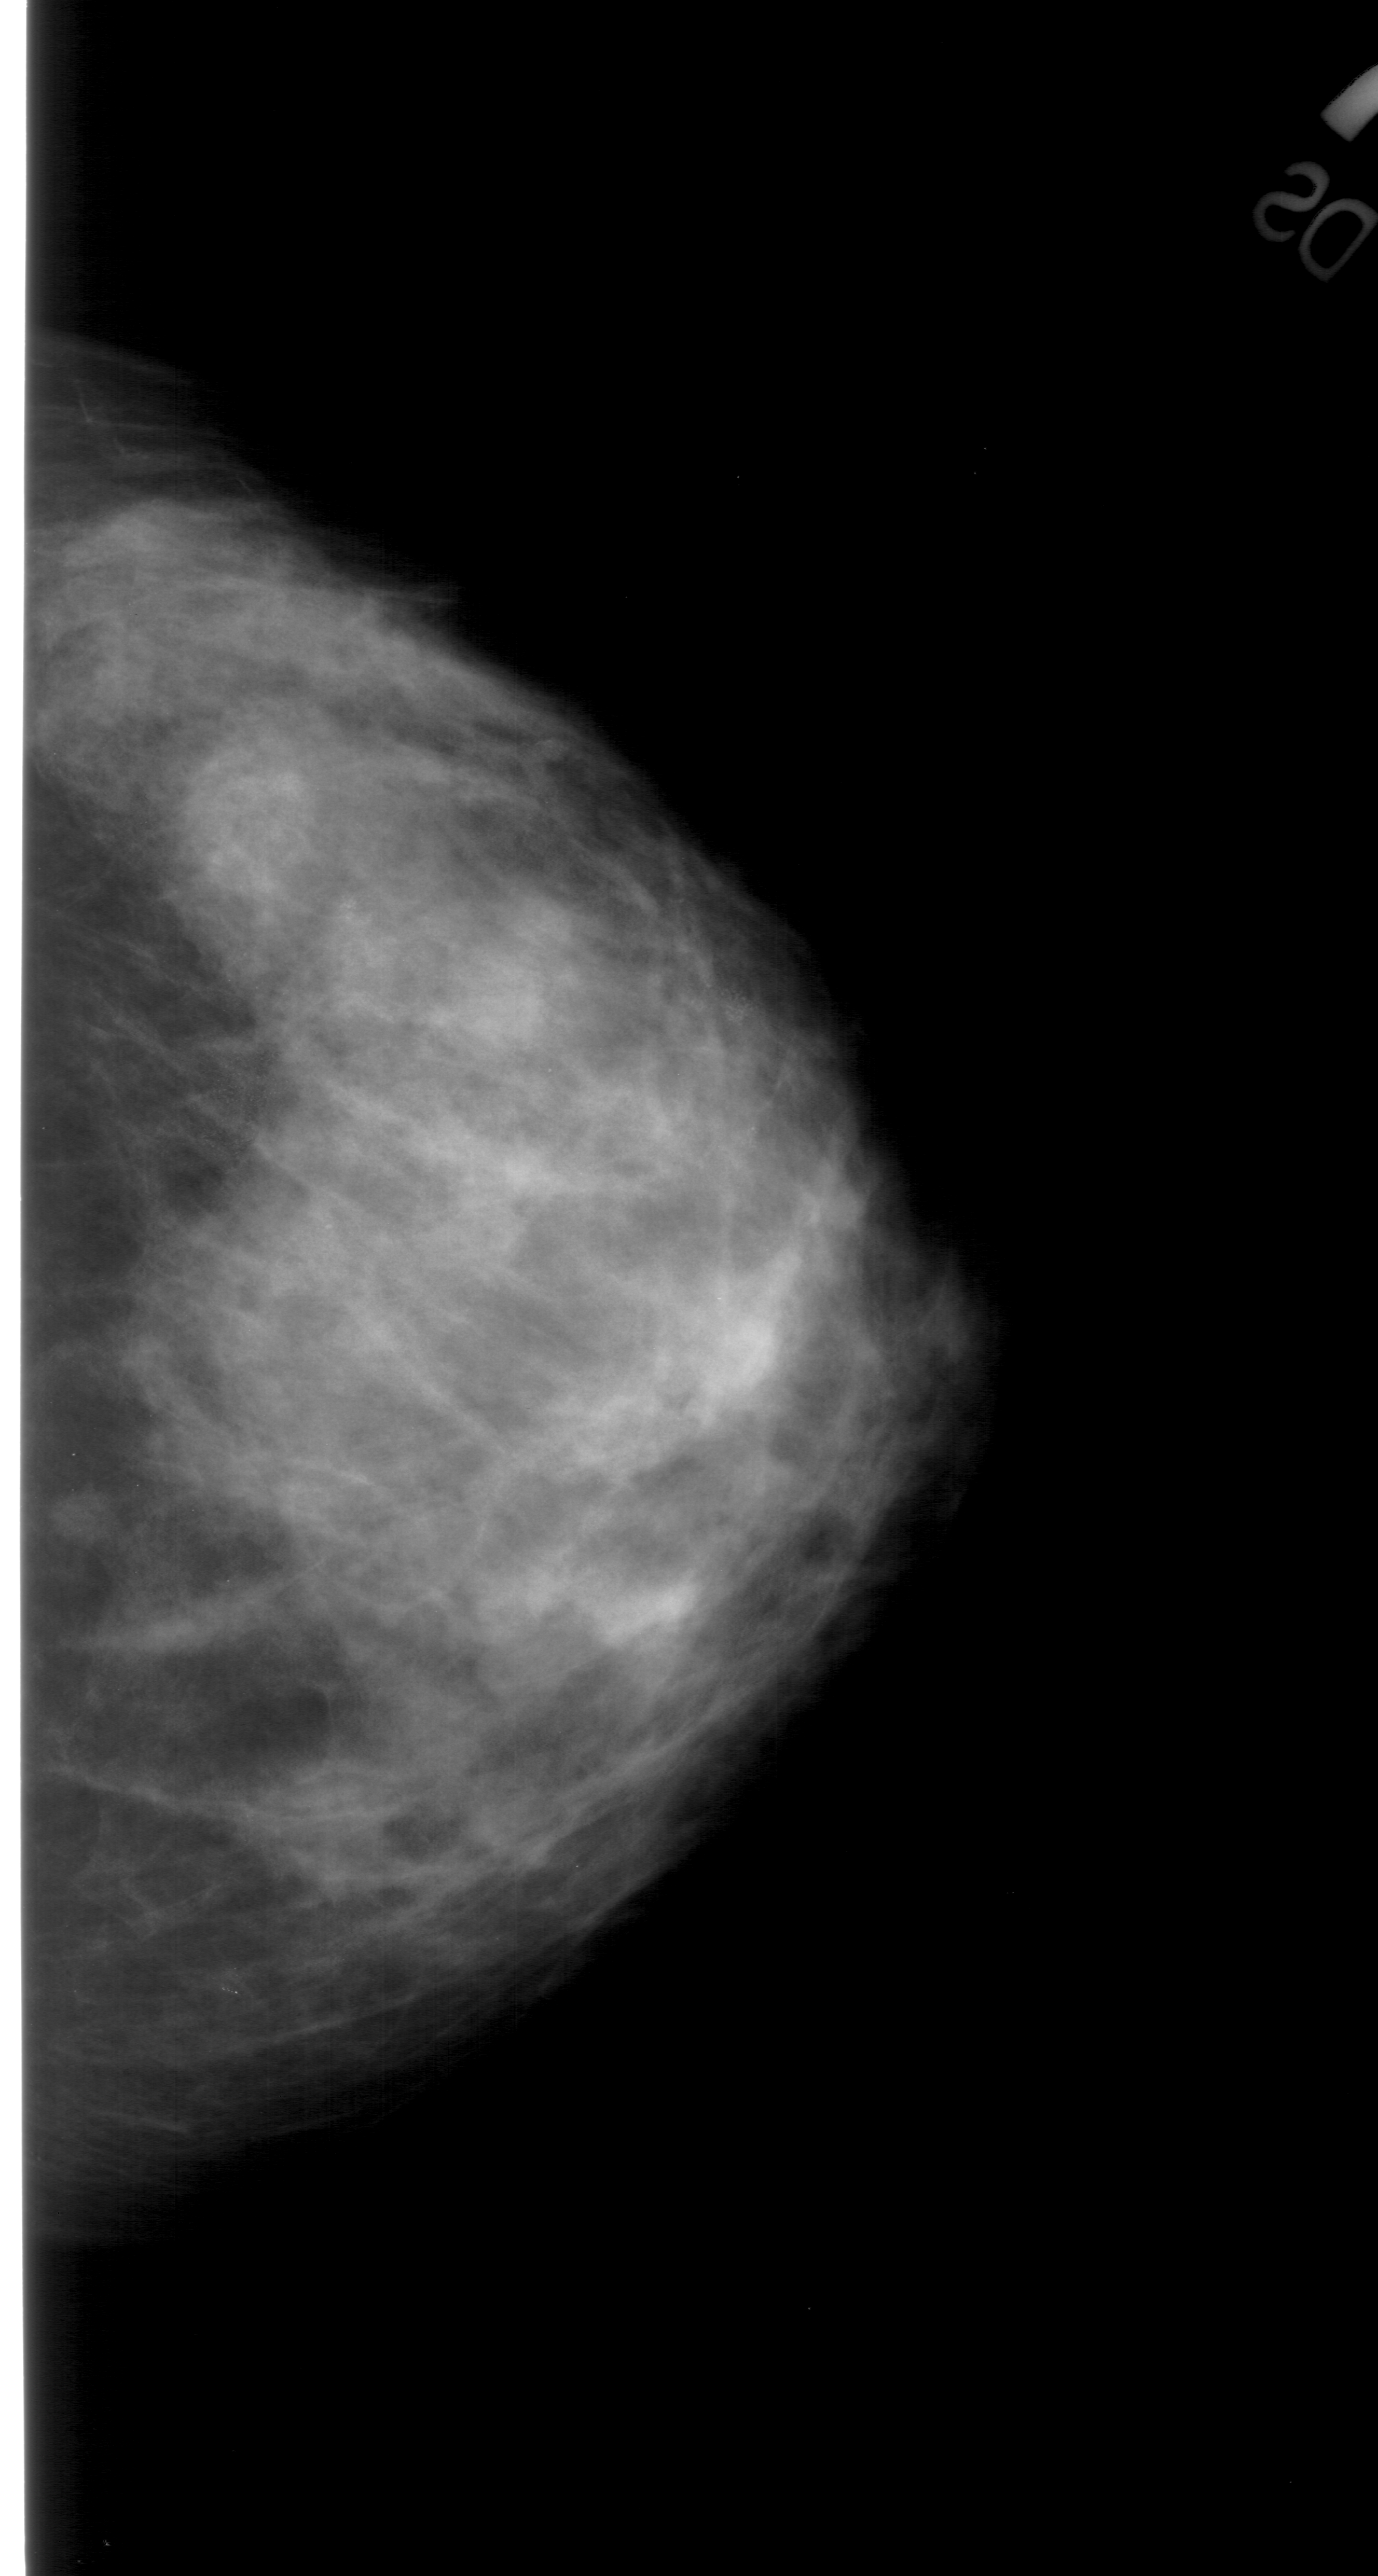
Mammogram (digitized film). Right breast. CC view. Breast composition: extremely dense (BI-RADS density category 4 of 4). 1378 × 2576 image matrix.
Expert-marked regions of interest on this film, with their recorded descriptors:
- calcifications, morphology pleomorphic, distribution segmental; BI-RADS assessment category 4; pathology (as recorded): malignant: bounding box [x1, y1, x2, y2] px = [159, 719, 875, 1306]